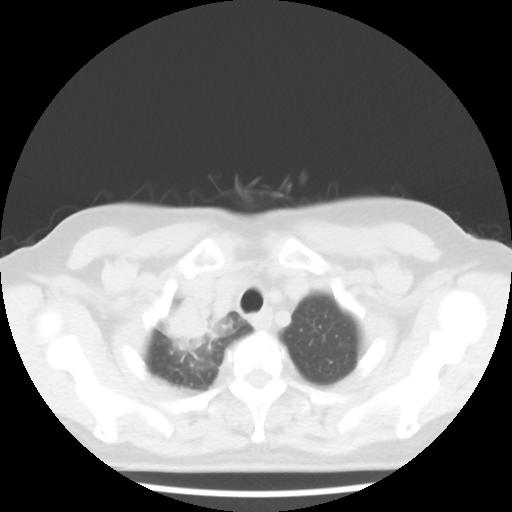
Chest CT, one axial slice. Slice 38 of 43 in the series (ordered by position). Lung window (W 1500 / L -600 HU). 5 mm slice thickness. 512 × 512 image matrix. Patient: female, 62 years. From the clinical record (not read from this slice): clinical TNM (as recorded): T3 N0 M0.
Structures marked on this image (rectangle marked by the reading radiologist):
- lung tumour (recorded histology: small cell carcinoma): bounding box (x1, y1, x2, y2) in pixels: (159, 289, 218, 354)